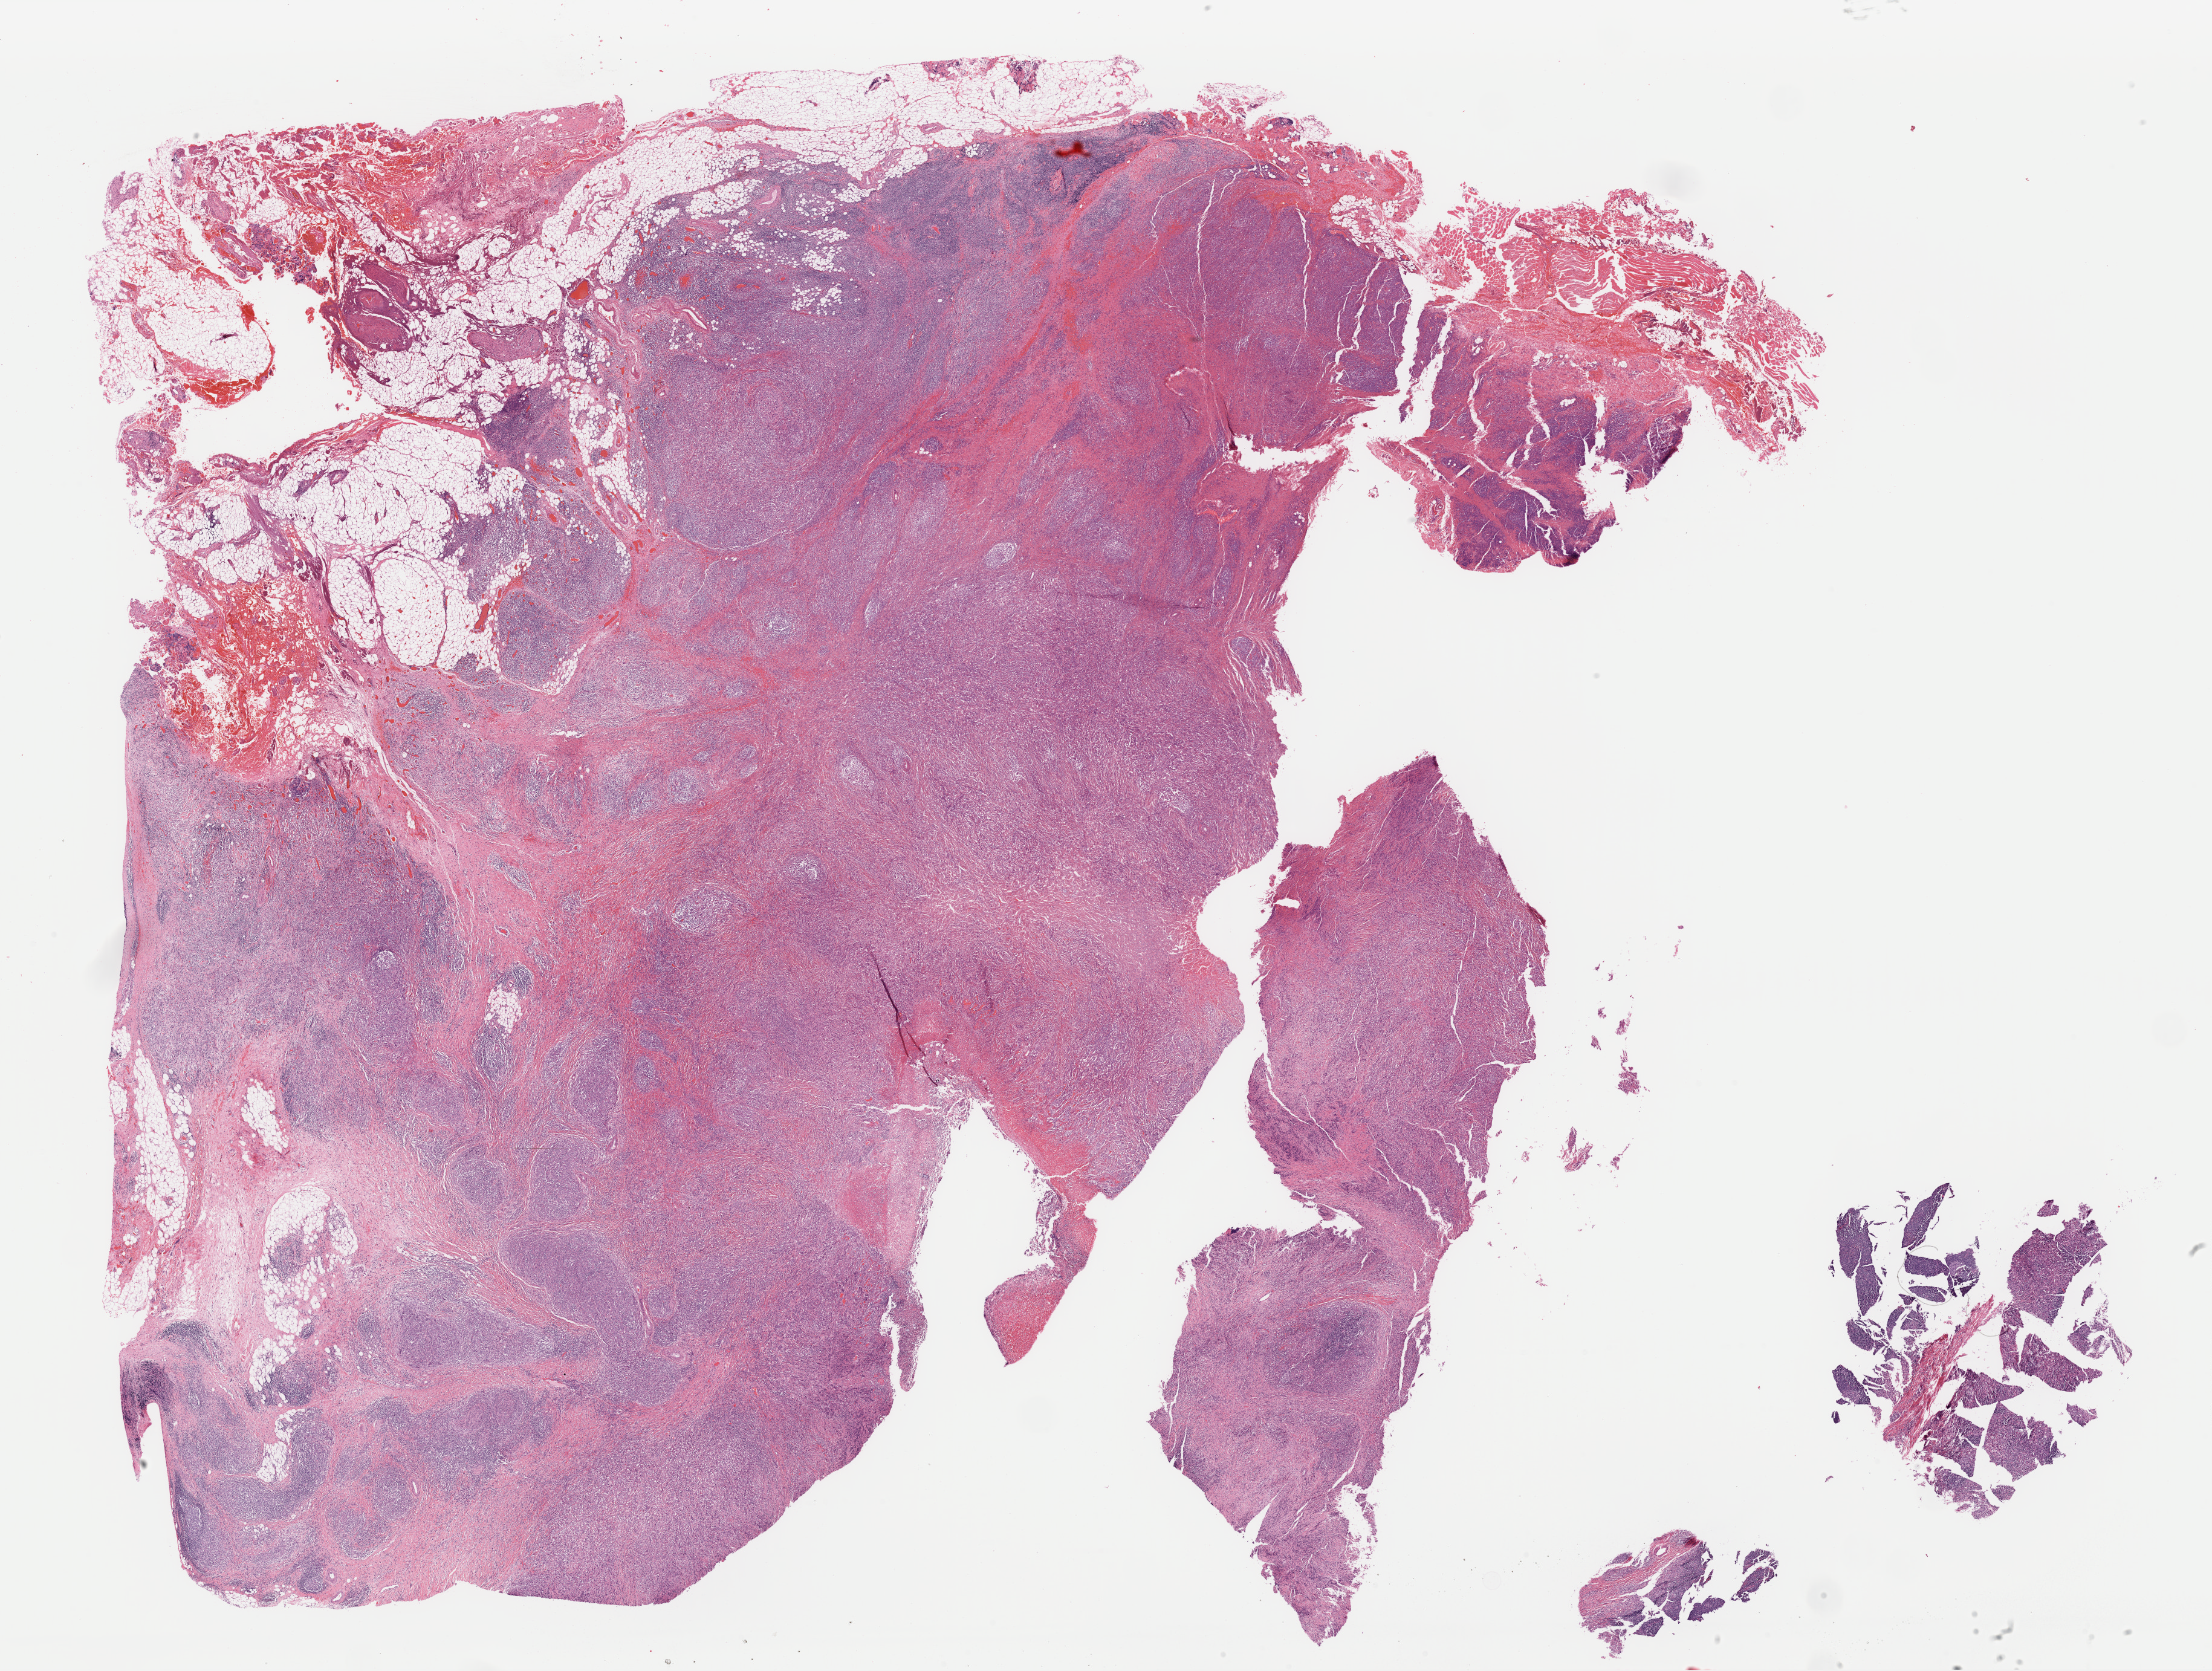
Digitized H&E-stained tissue section (whole slide) — whole scanned area (about 28.9 x 21.8 mm) shown as a low-resolution overview; formalin-fixed paraffin-embedded (FFPE) diagnostic section; esophagus, primary tumour sample. Female, age 50 years at initial diagnosis. Histologic grade: G2 (moderately differentiated).
• AJCC pathologic stage: IIIA (7th edition)
• histologic diagnosis: Adenocarcinoma, NOS (lower third of esophagus)